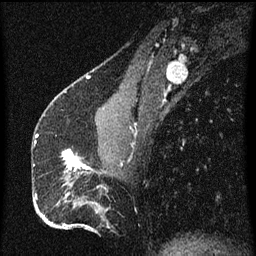
Breast MRI (dynamic contrast-enhanced), one sagittal slice; slice 26 of 60 in the series (ordered by position); dynamic contrast-enhanced series, image 2 of 3 at this slice position (ordered by acquisition); 1.5 T; TE 4.2 ms, TR 8 ms; 2 mm slice thickness; 256 × 256 image matrix. Female patient, age 51 years.
Structures marked on this image (semi-automatic segmentation, software-assisted and operator-edited):
- analysis volume of interest (the breast-tissue region the enhancement analysis was run in; not a lesion): bounding box <62,150,93,175> (left, top, right, bottom; pixels)
- tumour enhancement mask (voxels above the 70 % enhancement threshold inside the analysis volume of interest): <62,150,91,171>